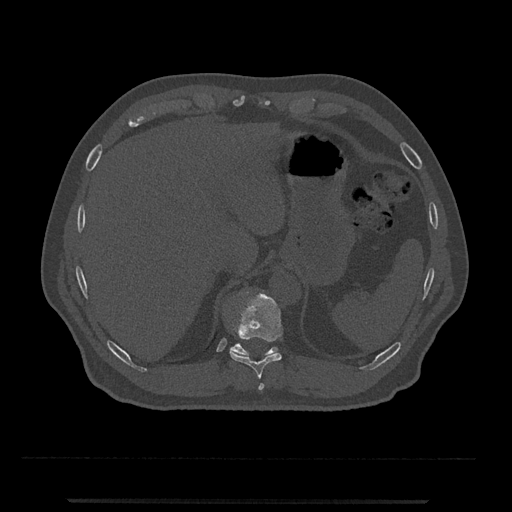
CT including the spine, one axial slice. Position 502 of 797 along the scan axis. Reconstruction kernel Br40s/3. 120 kVp. Bone window (W 1800 / L 400 HU). 0.5 mm slice thickness. 512 × 512 image matrix, field of view 419 × 419 mm. Patient: male, 63 years. Case-level facts recorded for this patient, not image findings: primary cancer: prostate.
Outlined on this slice (semi-automatically segmented with operator editing):
- T10 vertebra: bounding box (x1, y1, x2, y2) in pixels: (230, 291, 283, 379)
- T11 vertebra: (230, 343, 278, 356)
- T9 vertebra: (258, 383, 264, 390)